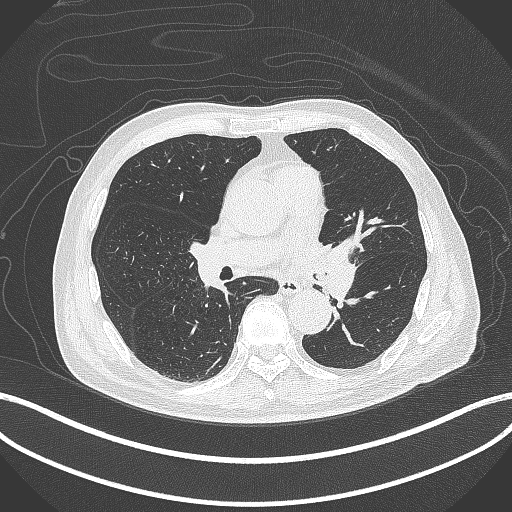
Chest CT, one axial slice; slice 229 of 417 in the series (ordered by position); reconstruction kernel B70f; 120 kVp; lung window (W 1500 / L -600 HU); 1 mm slice thickness; 512 × 512 image matrix. Male patient, age 77 years. From the clinical record (not read from this slice): clinical TNM (as recorded): T3 N1 M0.
Annotated regions visible in this slice (bounding box drawn by a radiologist):
- lung tumour (recorded histology: adenocarcinoma): bounding box <310,236,359,303> (left, top, right, bottom; pixels)